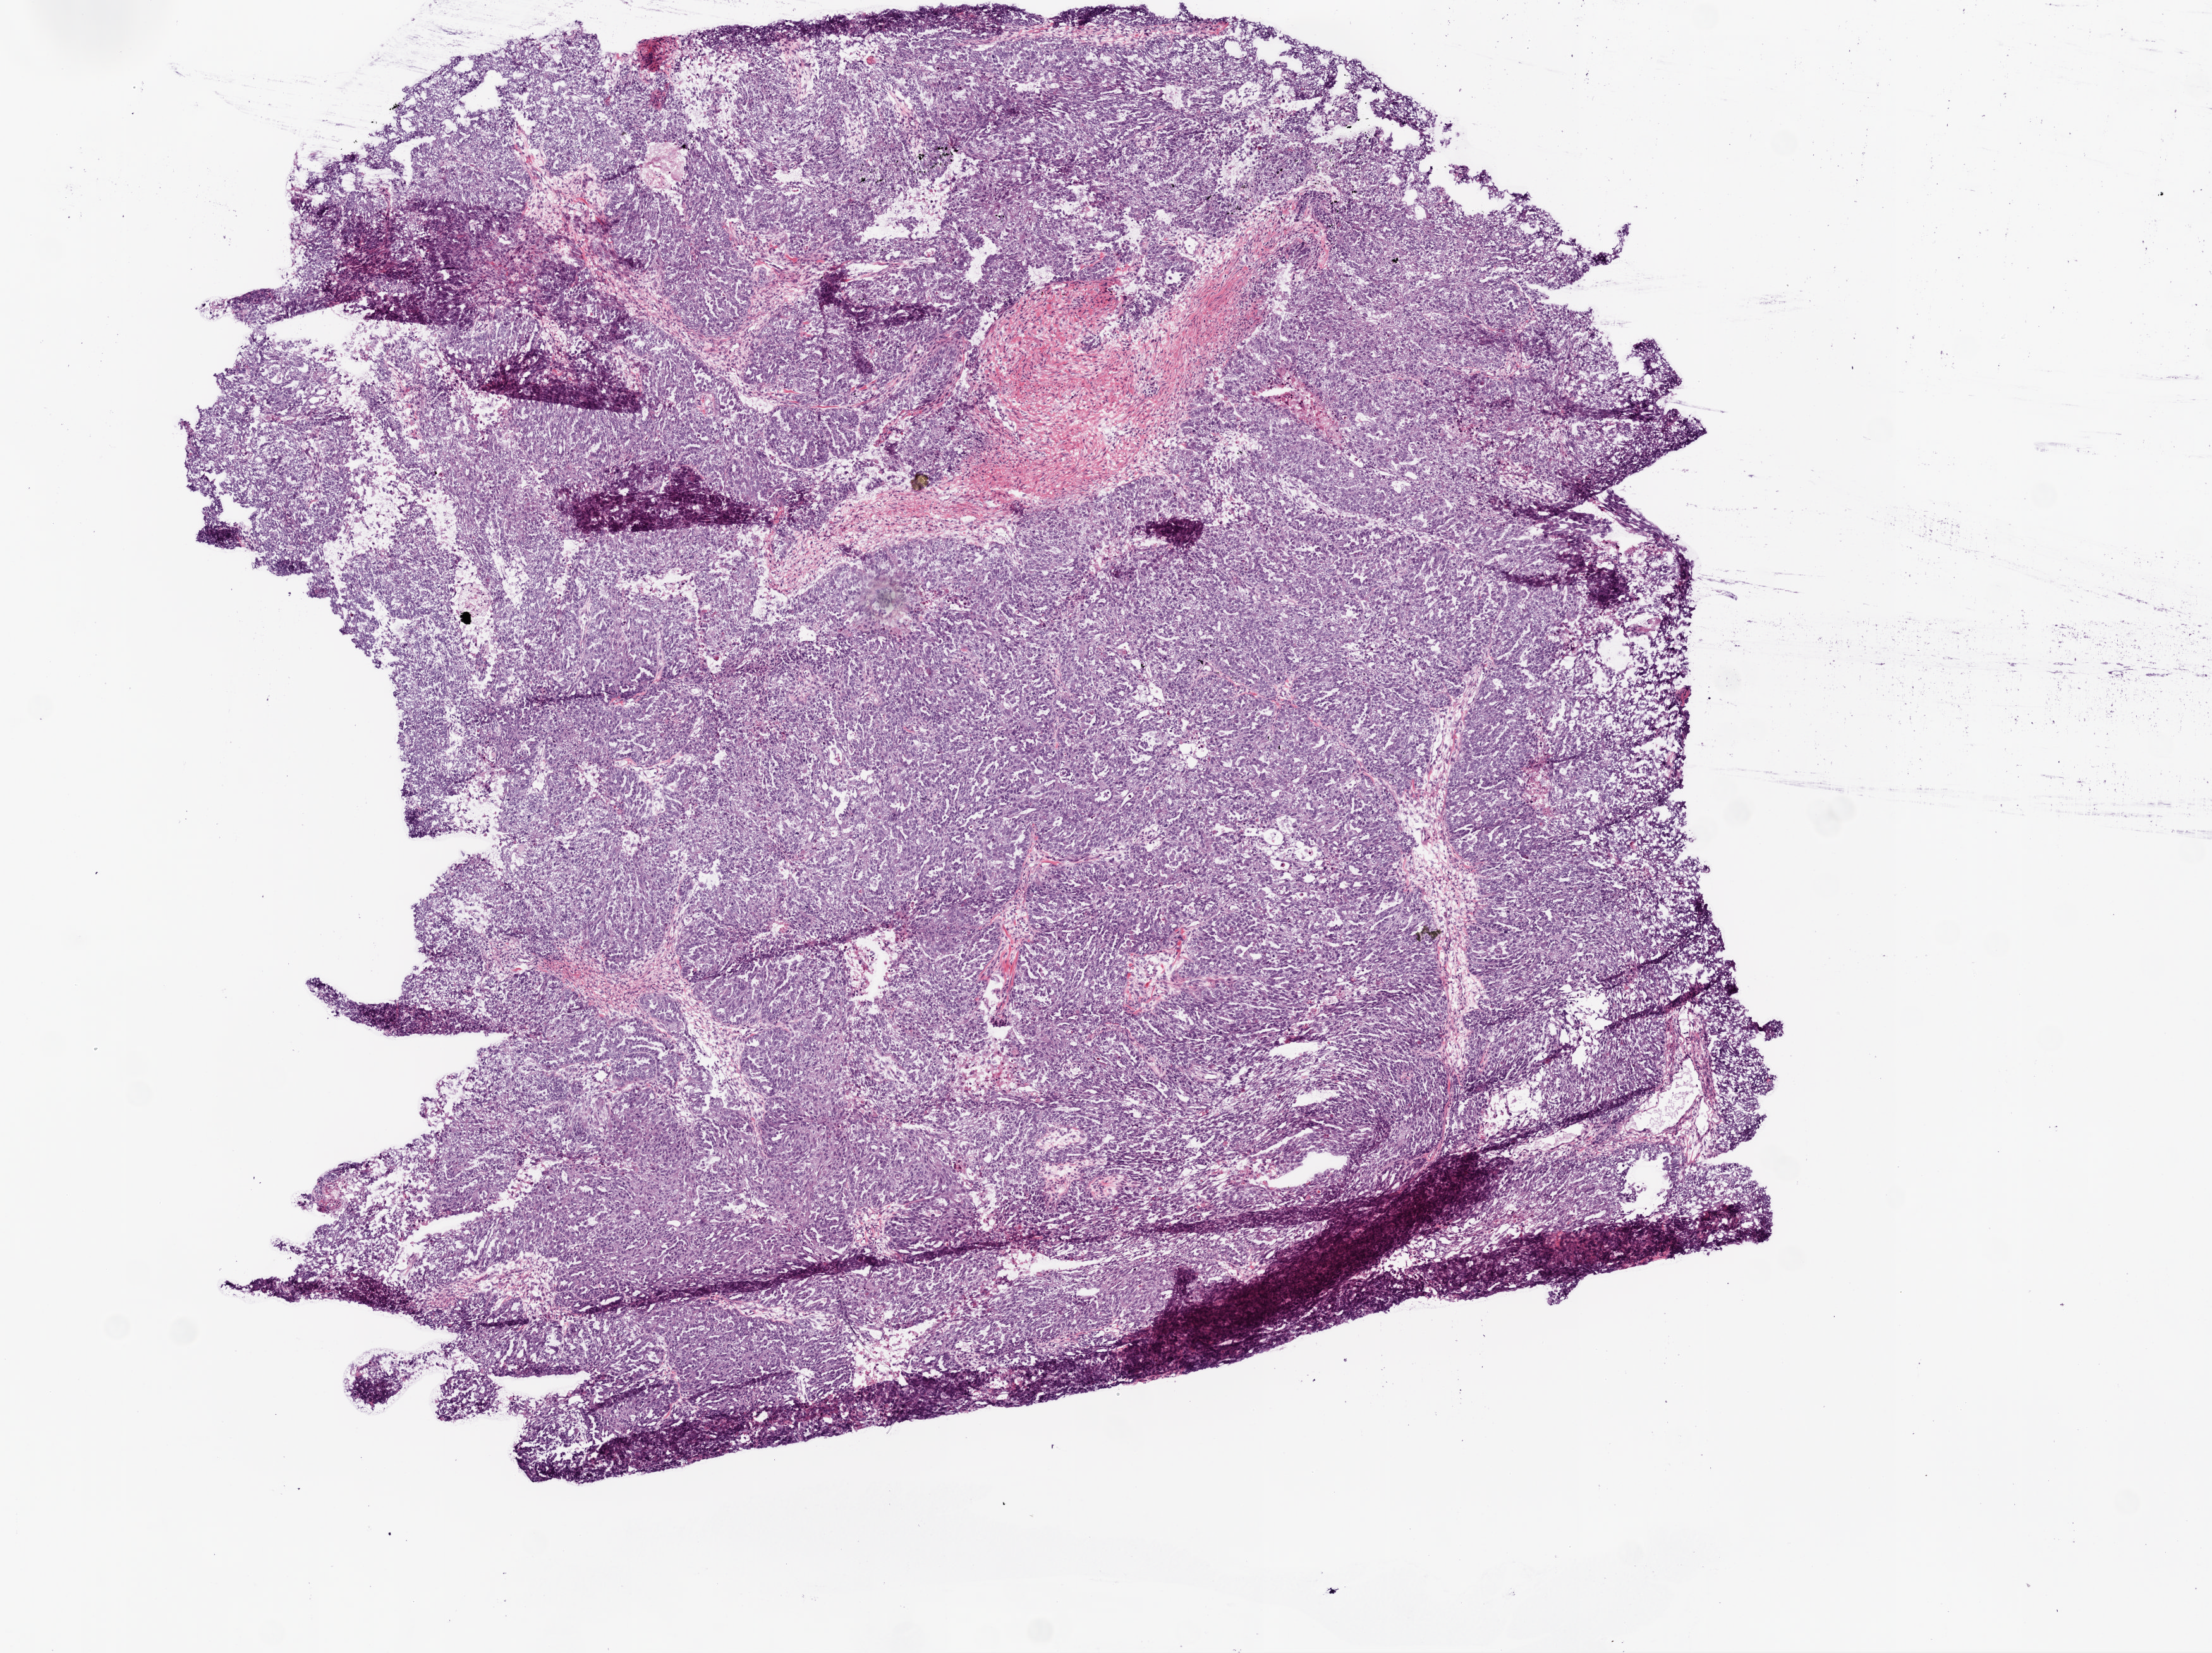
Digitized H&E-stained tissue section (whole slide), a low-resolution overview of the entire scanned area, about 7.0 x 5.2 mm (slide scanned at 20x). Frozen section from the top of the tissue portion. Sample: primary tumour, ovary. Female patient; age at initial diagnosis 53 years. Histologic grade: G3 (poorly differentiated). Slide review estimates, as recorded: tumour cells 94%, tumour nuclei 95%, normal cells 0%, stromal cells 5%, necrosis 1%.
• FIGO stage: IIIB
• diagnosis: Serous cystadenocarcinoma, NOS